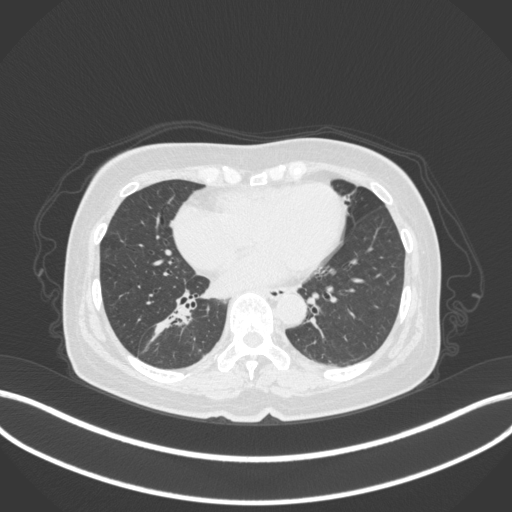
Chest CT, one axial slice. Slice 158 of 429 in the series (ordered by position). Reconstruction kernel B31f. 120 kVp. Lung window (W 1500 / L -600 HU). 512 × 512 image matrix. Female patient, age 67 years. Case-level facts recorded for this patient, not image findings: clinical TNM (as recorded): T1c N1 M0.
Outlined on this slice (bounding box drawn by a radiologist):
- lung tumour (recorded histology: adenocarcinoma): bounding box <151,301,195,340> (left, top, right, bottom; pixels)